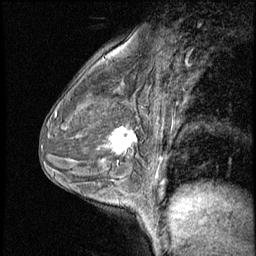
Breast MRI (dynamic contrast-enhanced), one sagittal slice; 3 images stored at this slice position (order not interpretable as contrast timing); 1.5 T; TE 4.2 ms, TR 8.7 ms; 2.5 mm slice thickness; 256 × 256 image matrix. Female patient, age 43 years. Case-level facts recorded for this patient, not image findings: setting: breast cancer imaged before/during neoadjuvant chemotherapy; receptor status: HR-positive, HER2-negative.
Outlined on this slice (semi-automatic segmentation, software-assisted and operator-edited):
- analysis volume of interest (the breast-tissue region the enhancement analysis was run in; not a lesion): box from (x=101, y=120) to (x=145, y=165) px
- tumour enhancement mask (voxels above the 140 % enhancement threshold inside the analysis volume of interest): (x=111, y=128)–(x=136, y=153)